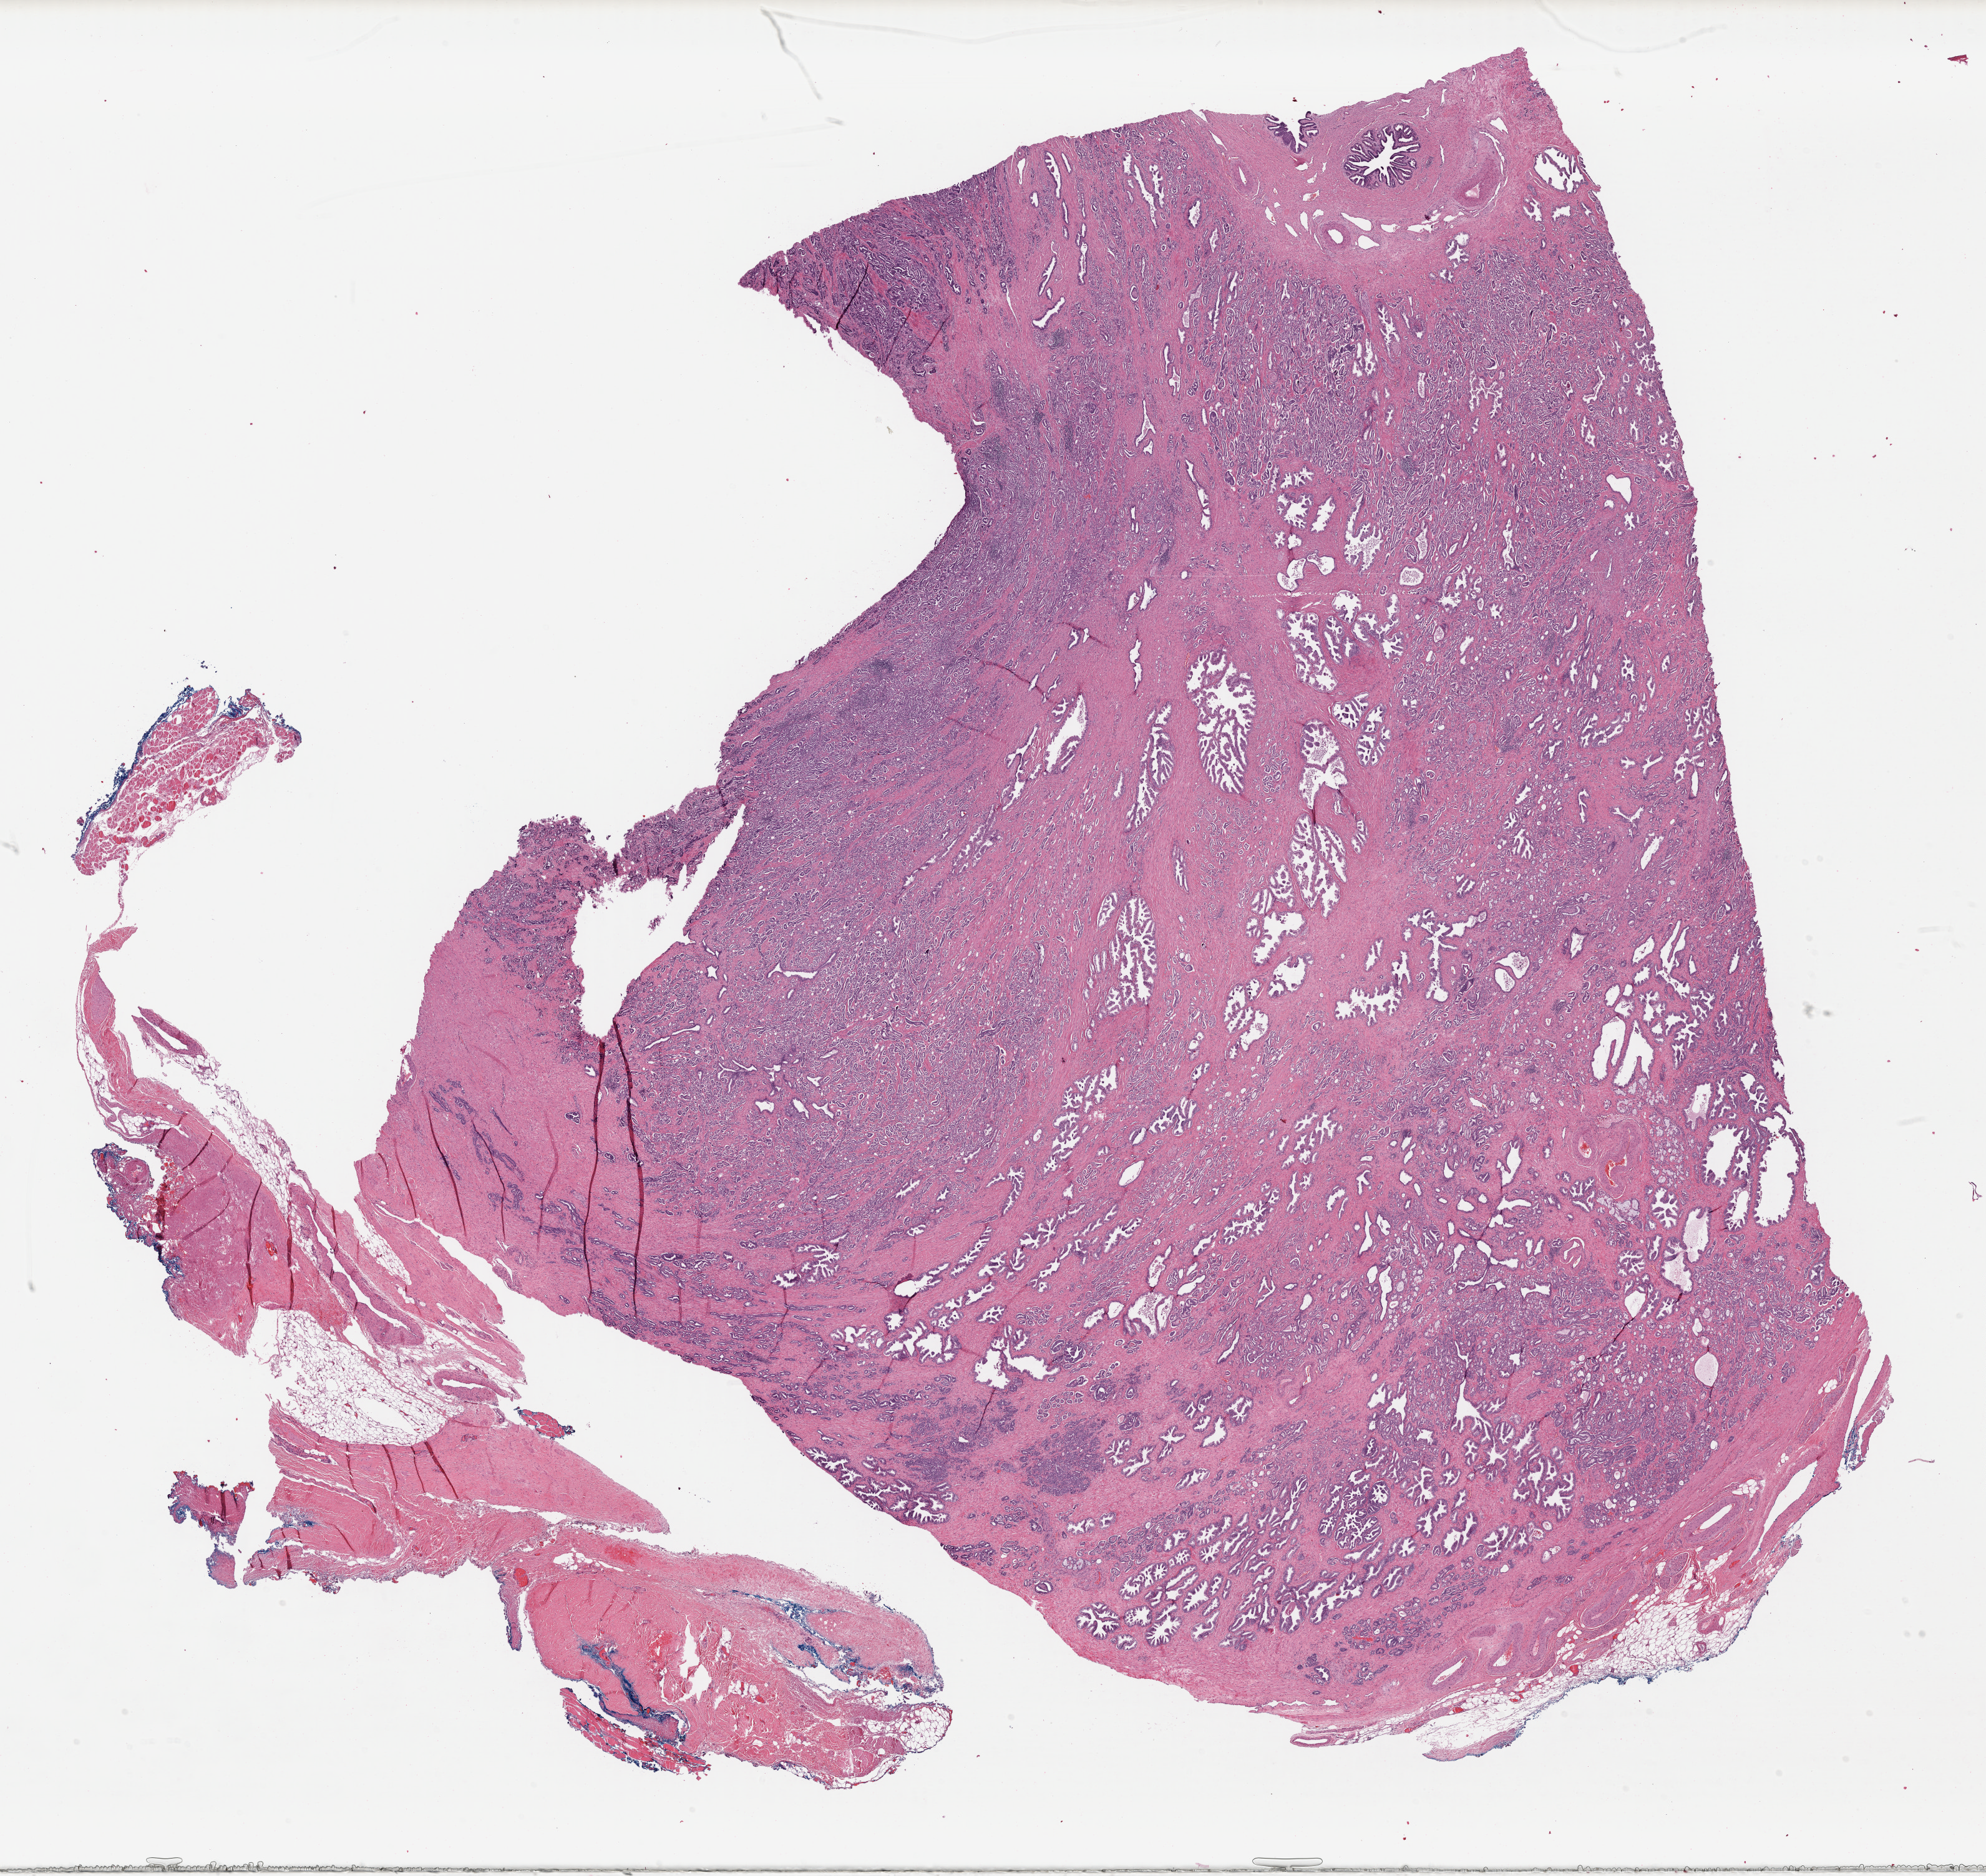
Digitized H&E tissue section (whole slide), low-resolution overview of the scanned area, about 25.0 x 23.6 mm, formalin-fixed paraffin-embedded (FFPE) diagnostic section, primary tumour sample from the prostate. Male, age 49 years at initial diagnosis. Gleason score: 7 (4+3).
Histologic diagnosis: Acinar cell carcinoma (prostate gland).